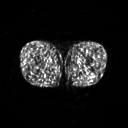
FDG PET of an extremity soft-tissue mass (from a PET/CT study), one axial slice; slice 226 of 267 in the series (ordered by position); 3.27 mm slice thickness; 128 × 128 image matrix, field of view 500 × 500 mm. Patient: male, 27 years. From the clinical record (not read from this slice): histological type: extraskeletal osteosarcoma; grade: high; site of the primary tumour: left adductur.
Annotated regions visible in this slice (expert contour drawn on MRI and transferred to this co-registered scan by the dataset authors):
- gross tumour volume (mass): box from (x=69, y=61) to (x=93, y=77) px